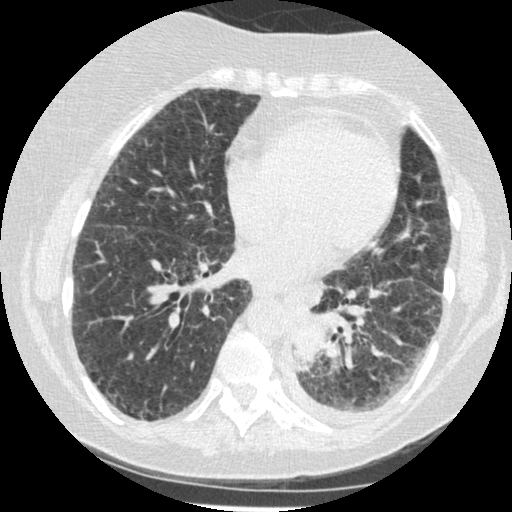
Low-dose screening chest CT, one axial slice. Position 84 of 341 along the scan axis. 120 kVp. Lung window (W 1500 / L -600 HU). 1.25 mm slice thickness. 512 × 512 image matrix, field of view 310 × 310 mm.
Annotated regions visible in this slice (manually delineated by an expert):
- lesion 1 (tumor, lower lobe of left lung): bounding box (x1, y1, x2, y2) in pixels: (291, 320, 323, 371)